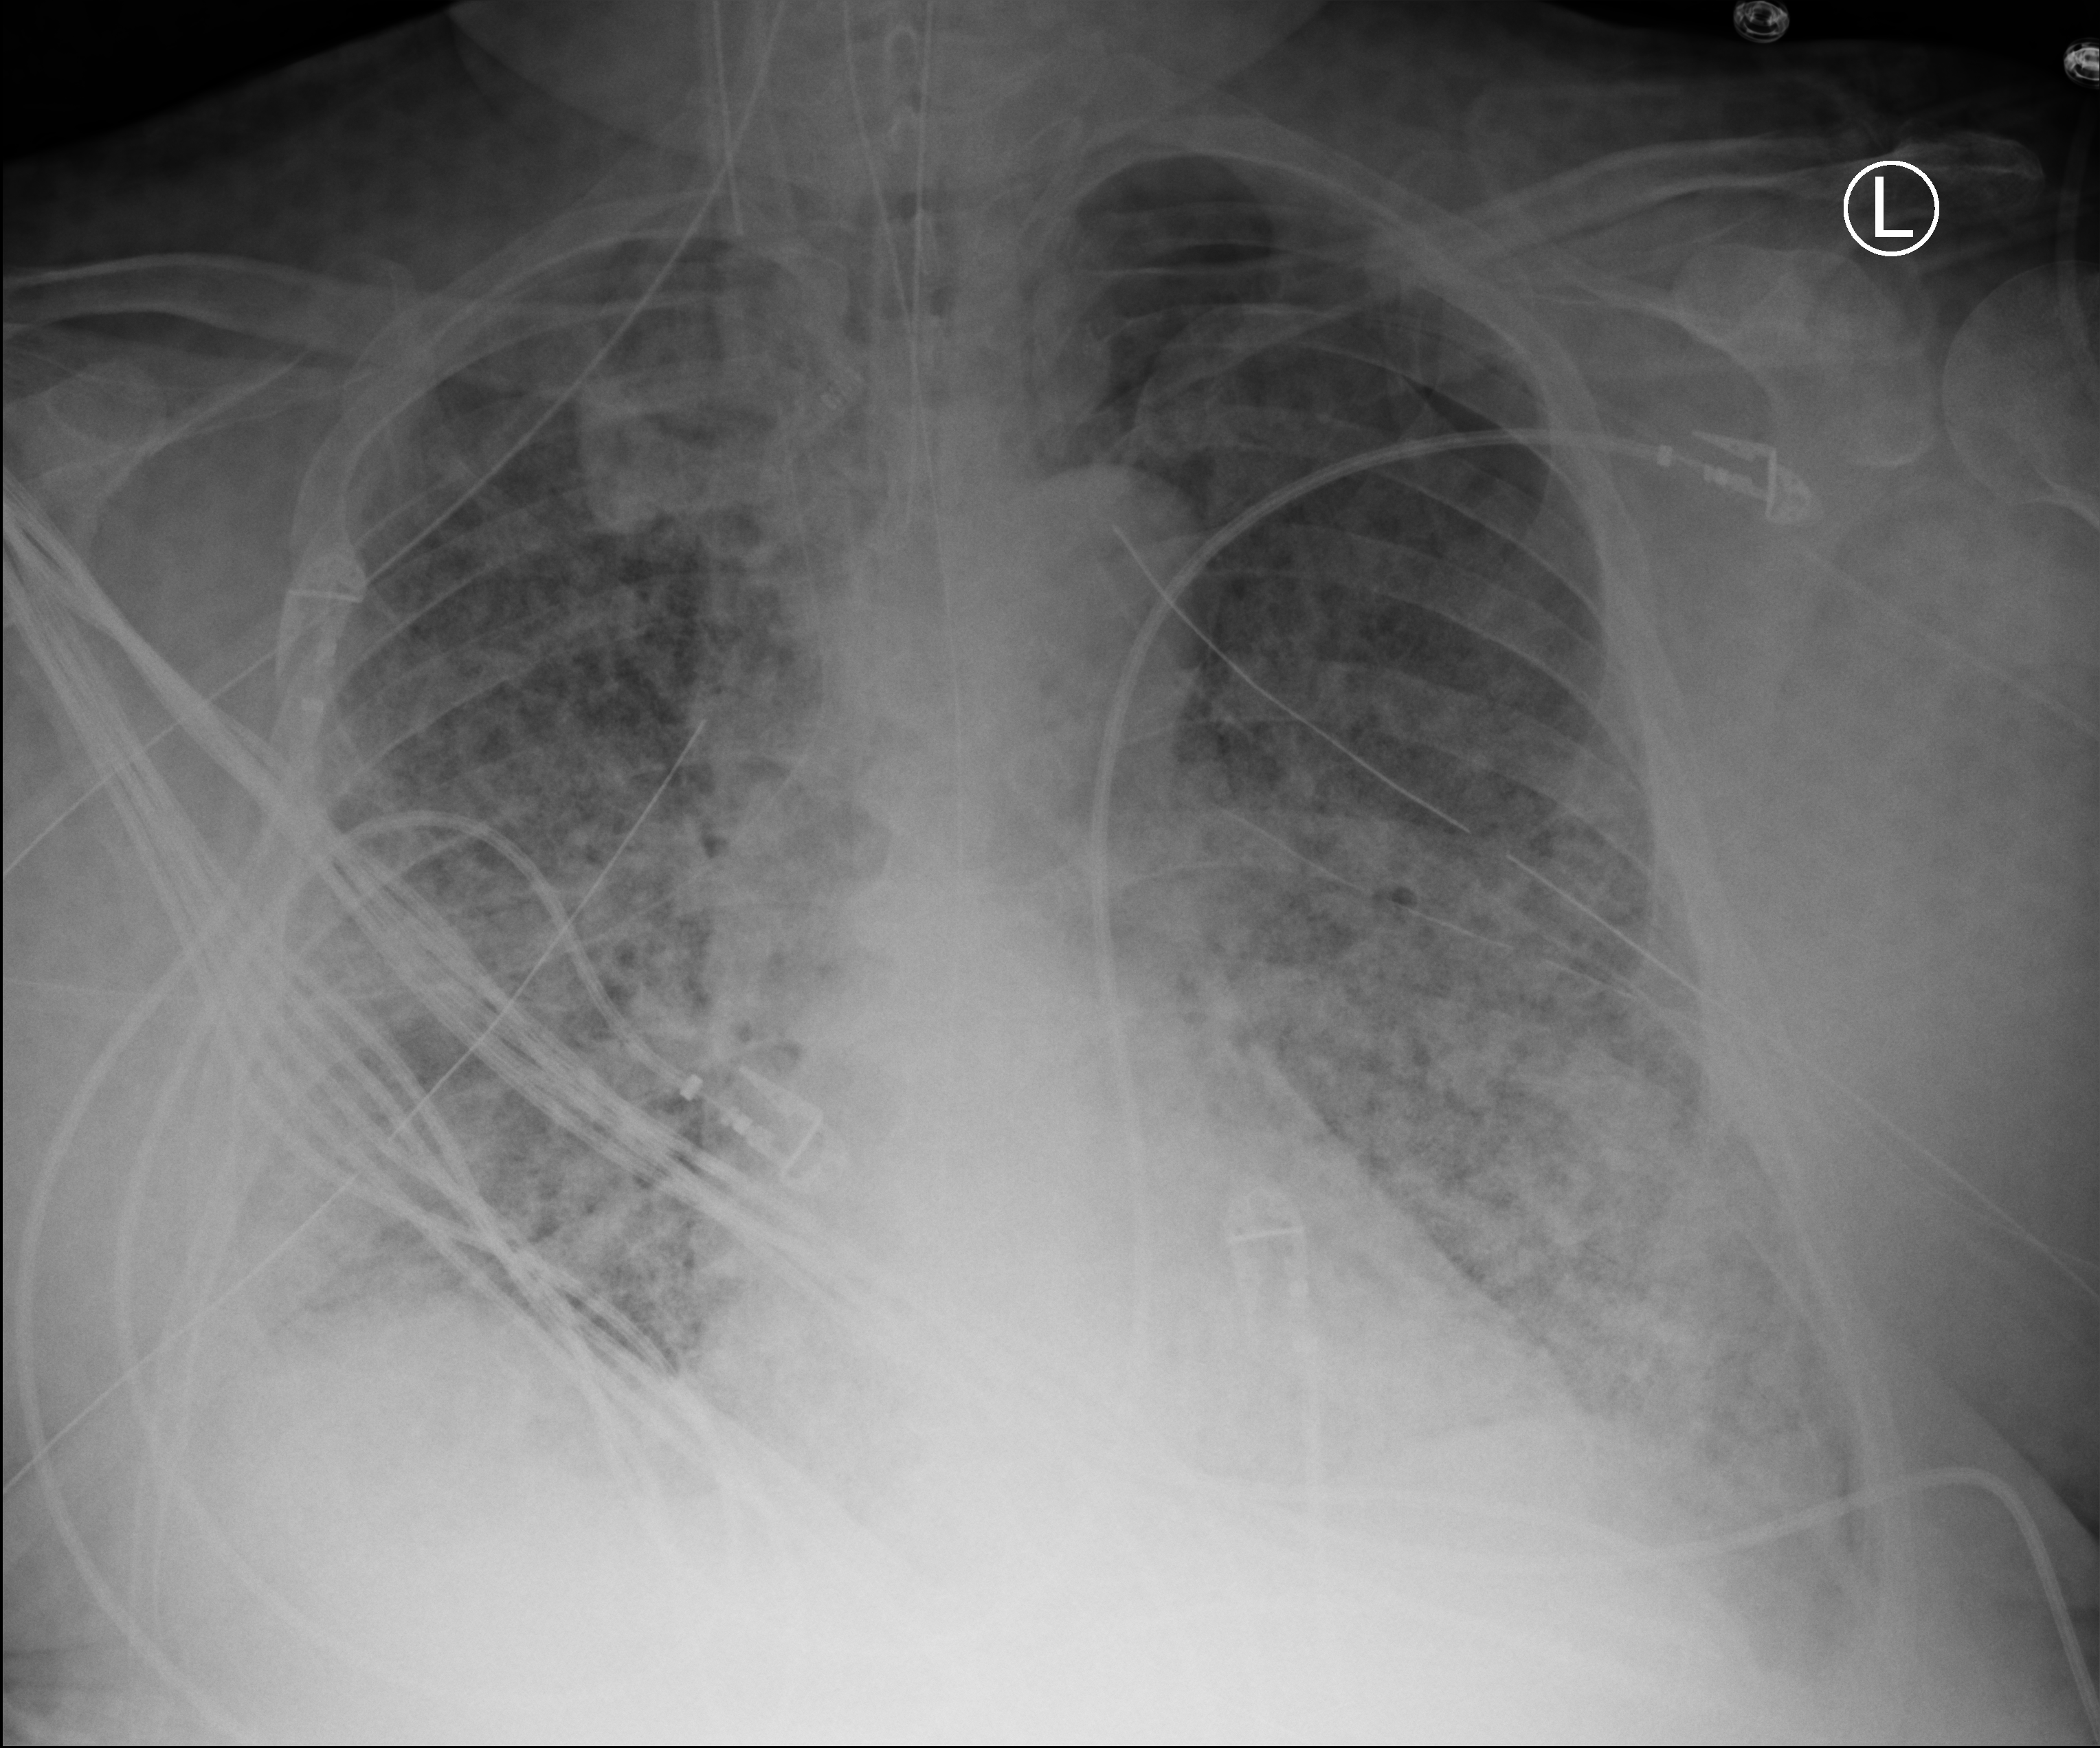
Portable chest radiograph, anteroposterior (AP) projection. Patient hospitalised with COVID-19, aged 18–59 years.
Admission-level facts for this patient (not findings on this image; timing relative to this image not recorded):
- hypertension (admission record): yes
- length of hospital stay: 28 days